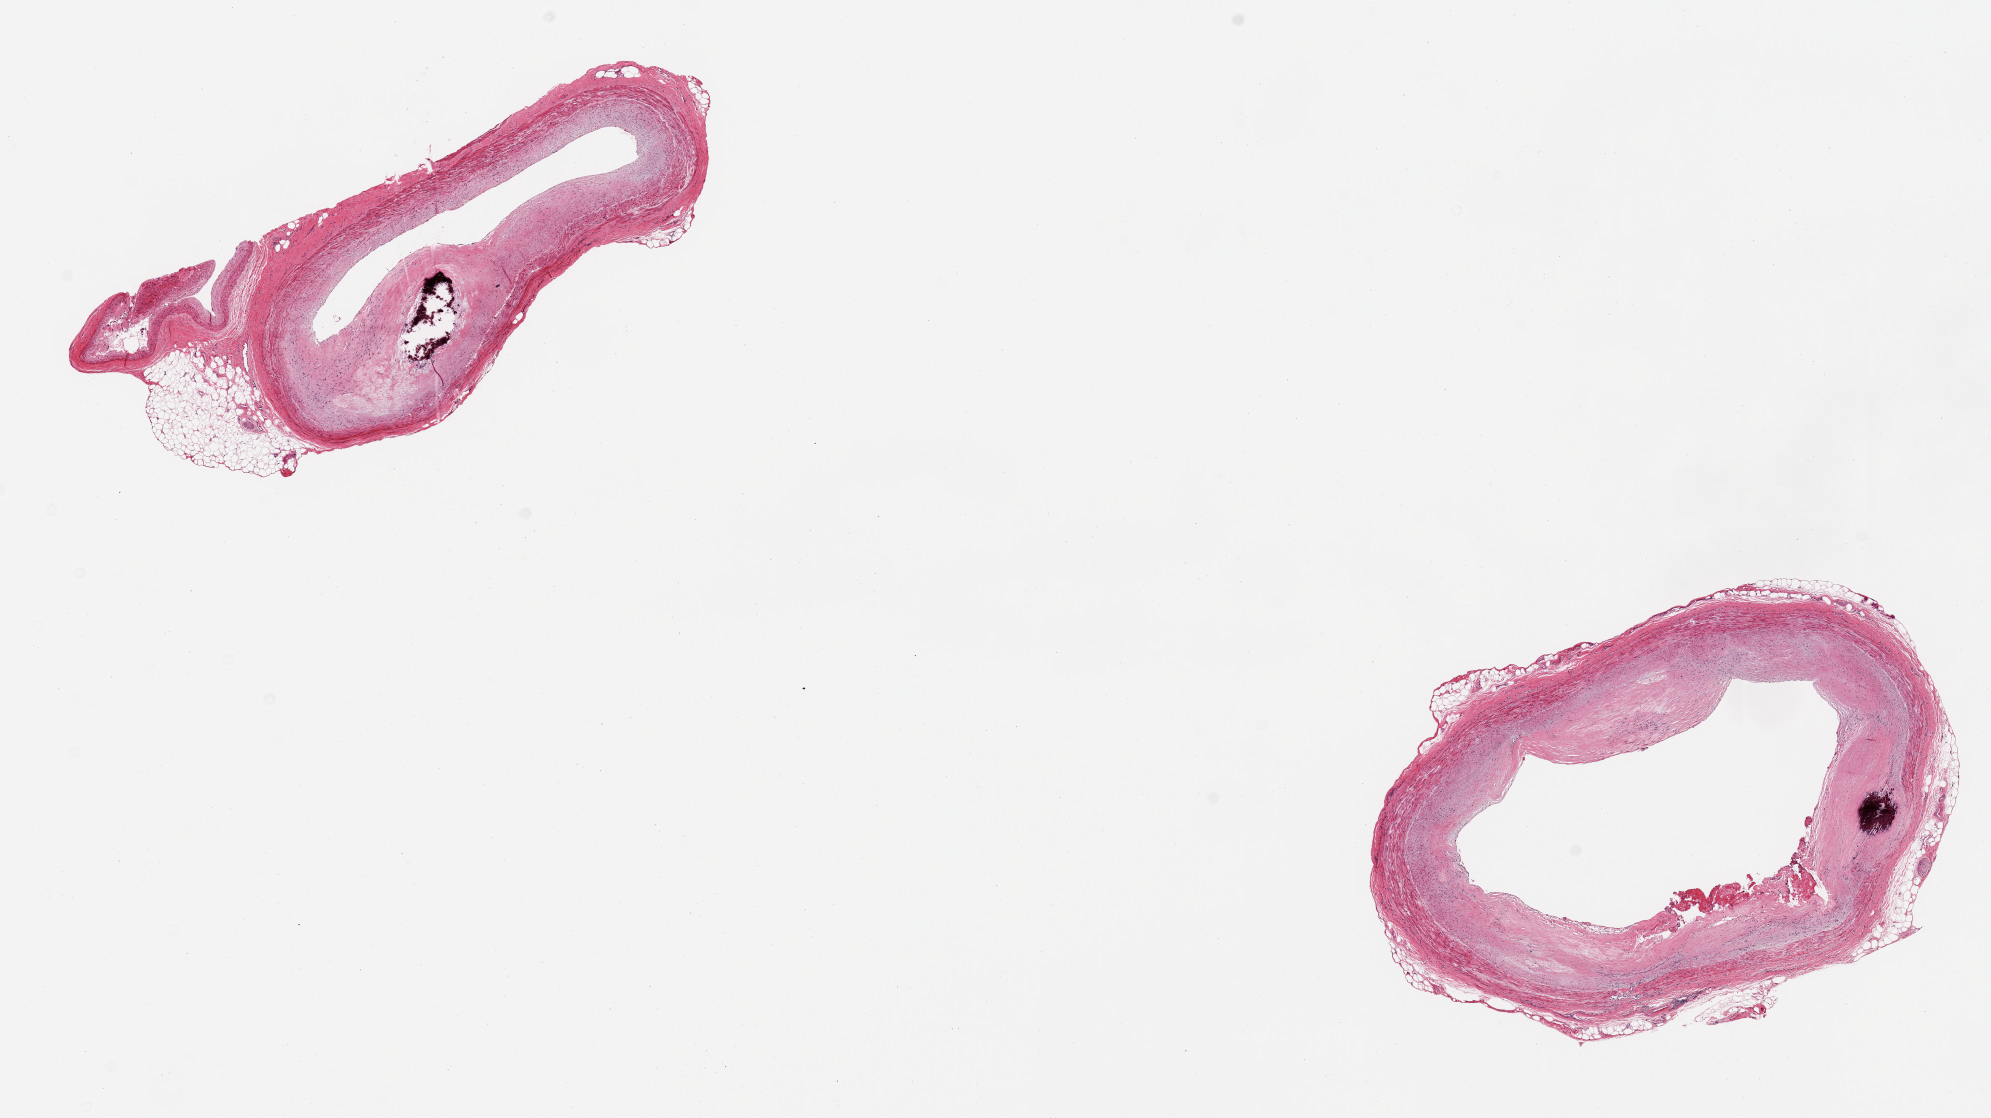
Digitized hematoxylin and eosin (H&E)-stained section — a low-resolution overview of the entire scanned area, about 15.8 x 8.8 mm, PAXgene-fixed paraffin-embedded (PFPE) section, target tissue: coronary artery, tissue donor sample. Donor: male.
Reviewer comment on this tissue sample: 2 pieces, ~50% occlusive atherosis, focally calcified.